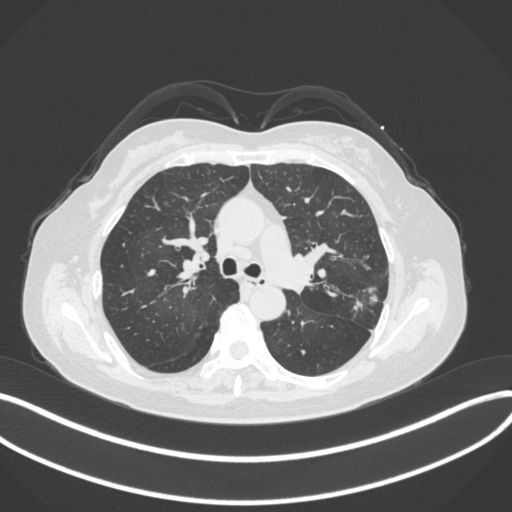
Chest CT, one axial slice; slice 216 of 330 in the series (ordered by position); reconstruction kernel B31f; lung window (W 1500 / L -600 HU); 1 mm slice thickness; 512 × 512 image matrix, field of view 400 × 400 mm. Female patient, age 60 years. Case-level facts recorded for this patient, not image findings: clinical TNM (as recorded): T1c N0 M0.
Annotated regions visible in this slice (bounding box drawn by a radiologist):
- lung tumour (recorded histology: adenocarcinoma): bounding box (x1, y1, x2, y2) in pixels: (351, 281, 381, 314)